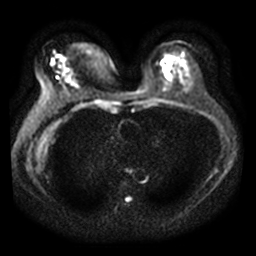
Breast MRI, one axial slice. Position 21 of 40 along the scan axis. Diffusion-weighted series; image 2 of 4 stored at this slice position (different b-values; order by instance number). 3 T. 5 mm slice thickness. 256 × 256 image matrix, field of view 340 × 340 mm. Female patient.
Outlined on this slice (expert manual segmentation):
- tumour on diffusion-weighted imaging: box from (x=57, y=54) to (x=61, y=57) px